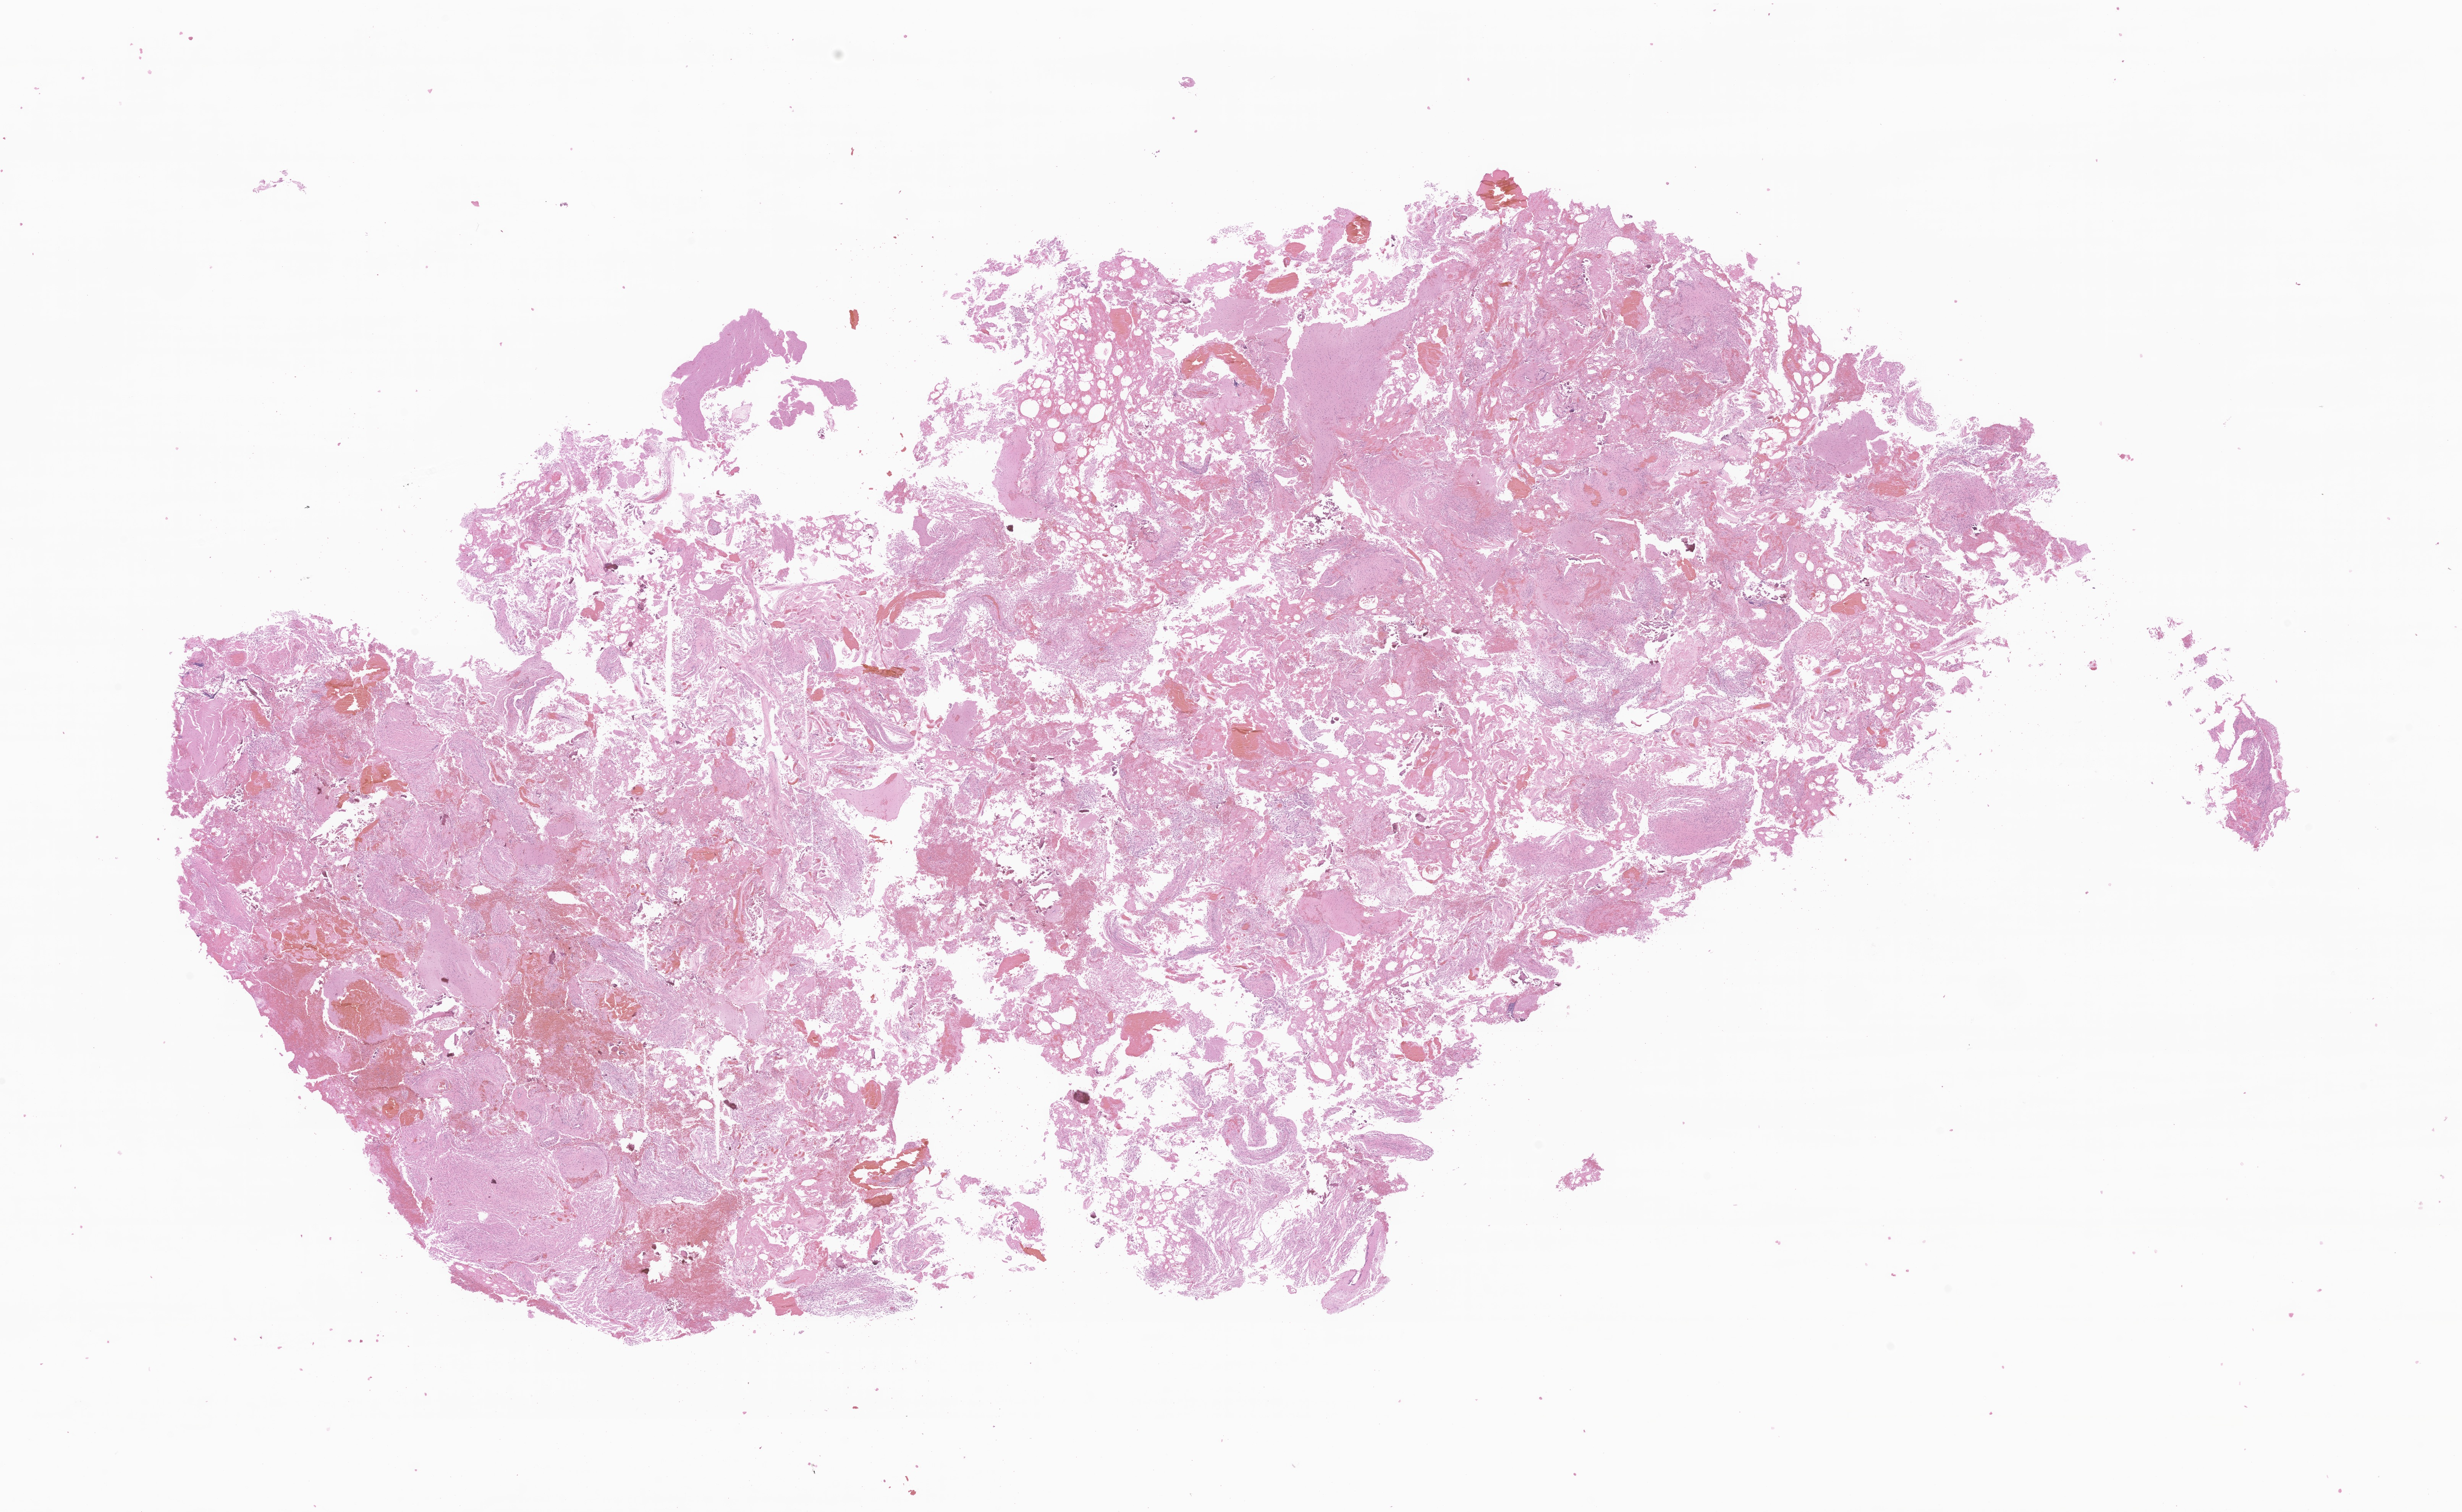
Haematoxylin and eosin whole-slide image of tumor tissue from the brain, shown as a low-resolution overview of the whole scanned area (about 27.2 x 16.7 mm); FFPE section. Patient male; age 64 months (5 years 4 months).
Recorded diagnosis: Pilocytic astrocytoma.